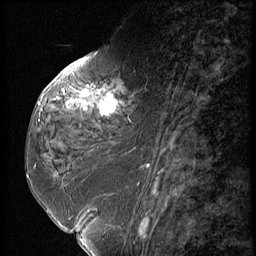
Breast MRI (dynamic contrast-enhanced), one sagittal slice; slice 25 of 56 in the series (ordered by position); dynamic contrast-enhanced series, image 2 of 3 at this slice position (ordered by acquisition); 1.5 T; TE 4.2 ms, TR 9 ms; 256 × 256 image matrix, field of view 180 × 180 mm. Patient: female, 59 years. From the clinical record (not read from this slice): setting: breast cancer imaged before/during neoadjuvant chemotherapy; receptor status: HER2-positive.
Outlined on this slice (semi-automatic segmentation, software-assisted and operator-edited):
- analysis volume of interest (the breast-tissue region the enhancement analysis was run in; not a lesion): box from (x=44, y=66) to (x=151, y=135) px
- tumour enhancement mask (voxels above the 140 % enhancement threshold inside the analysis volume of interest): (x=65, y=81)–(x=120, y=115)